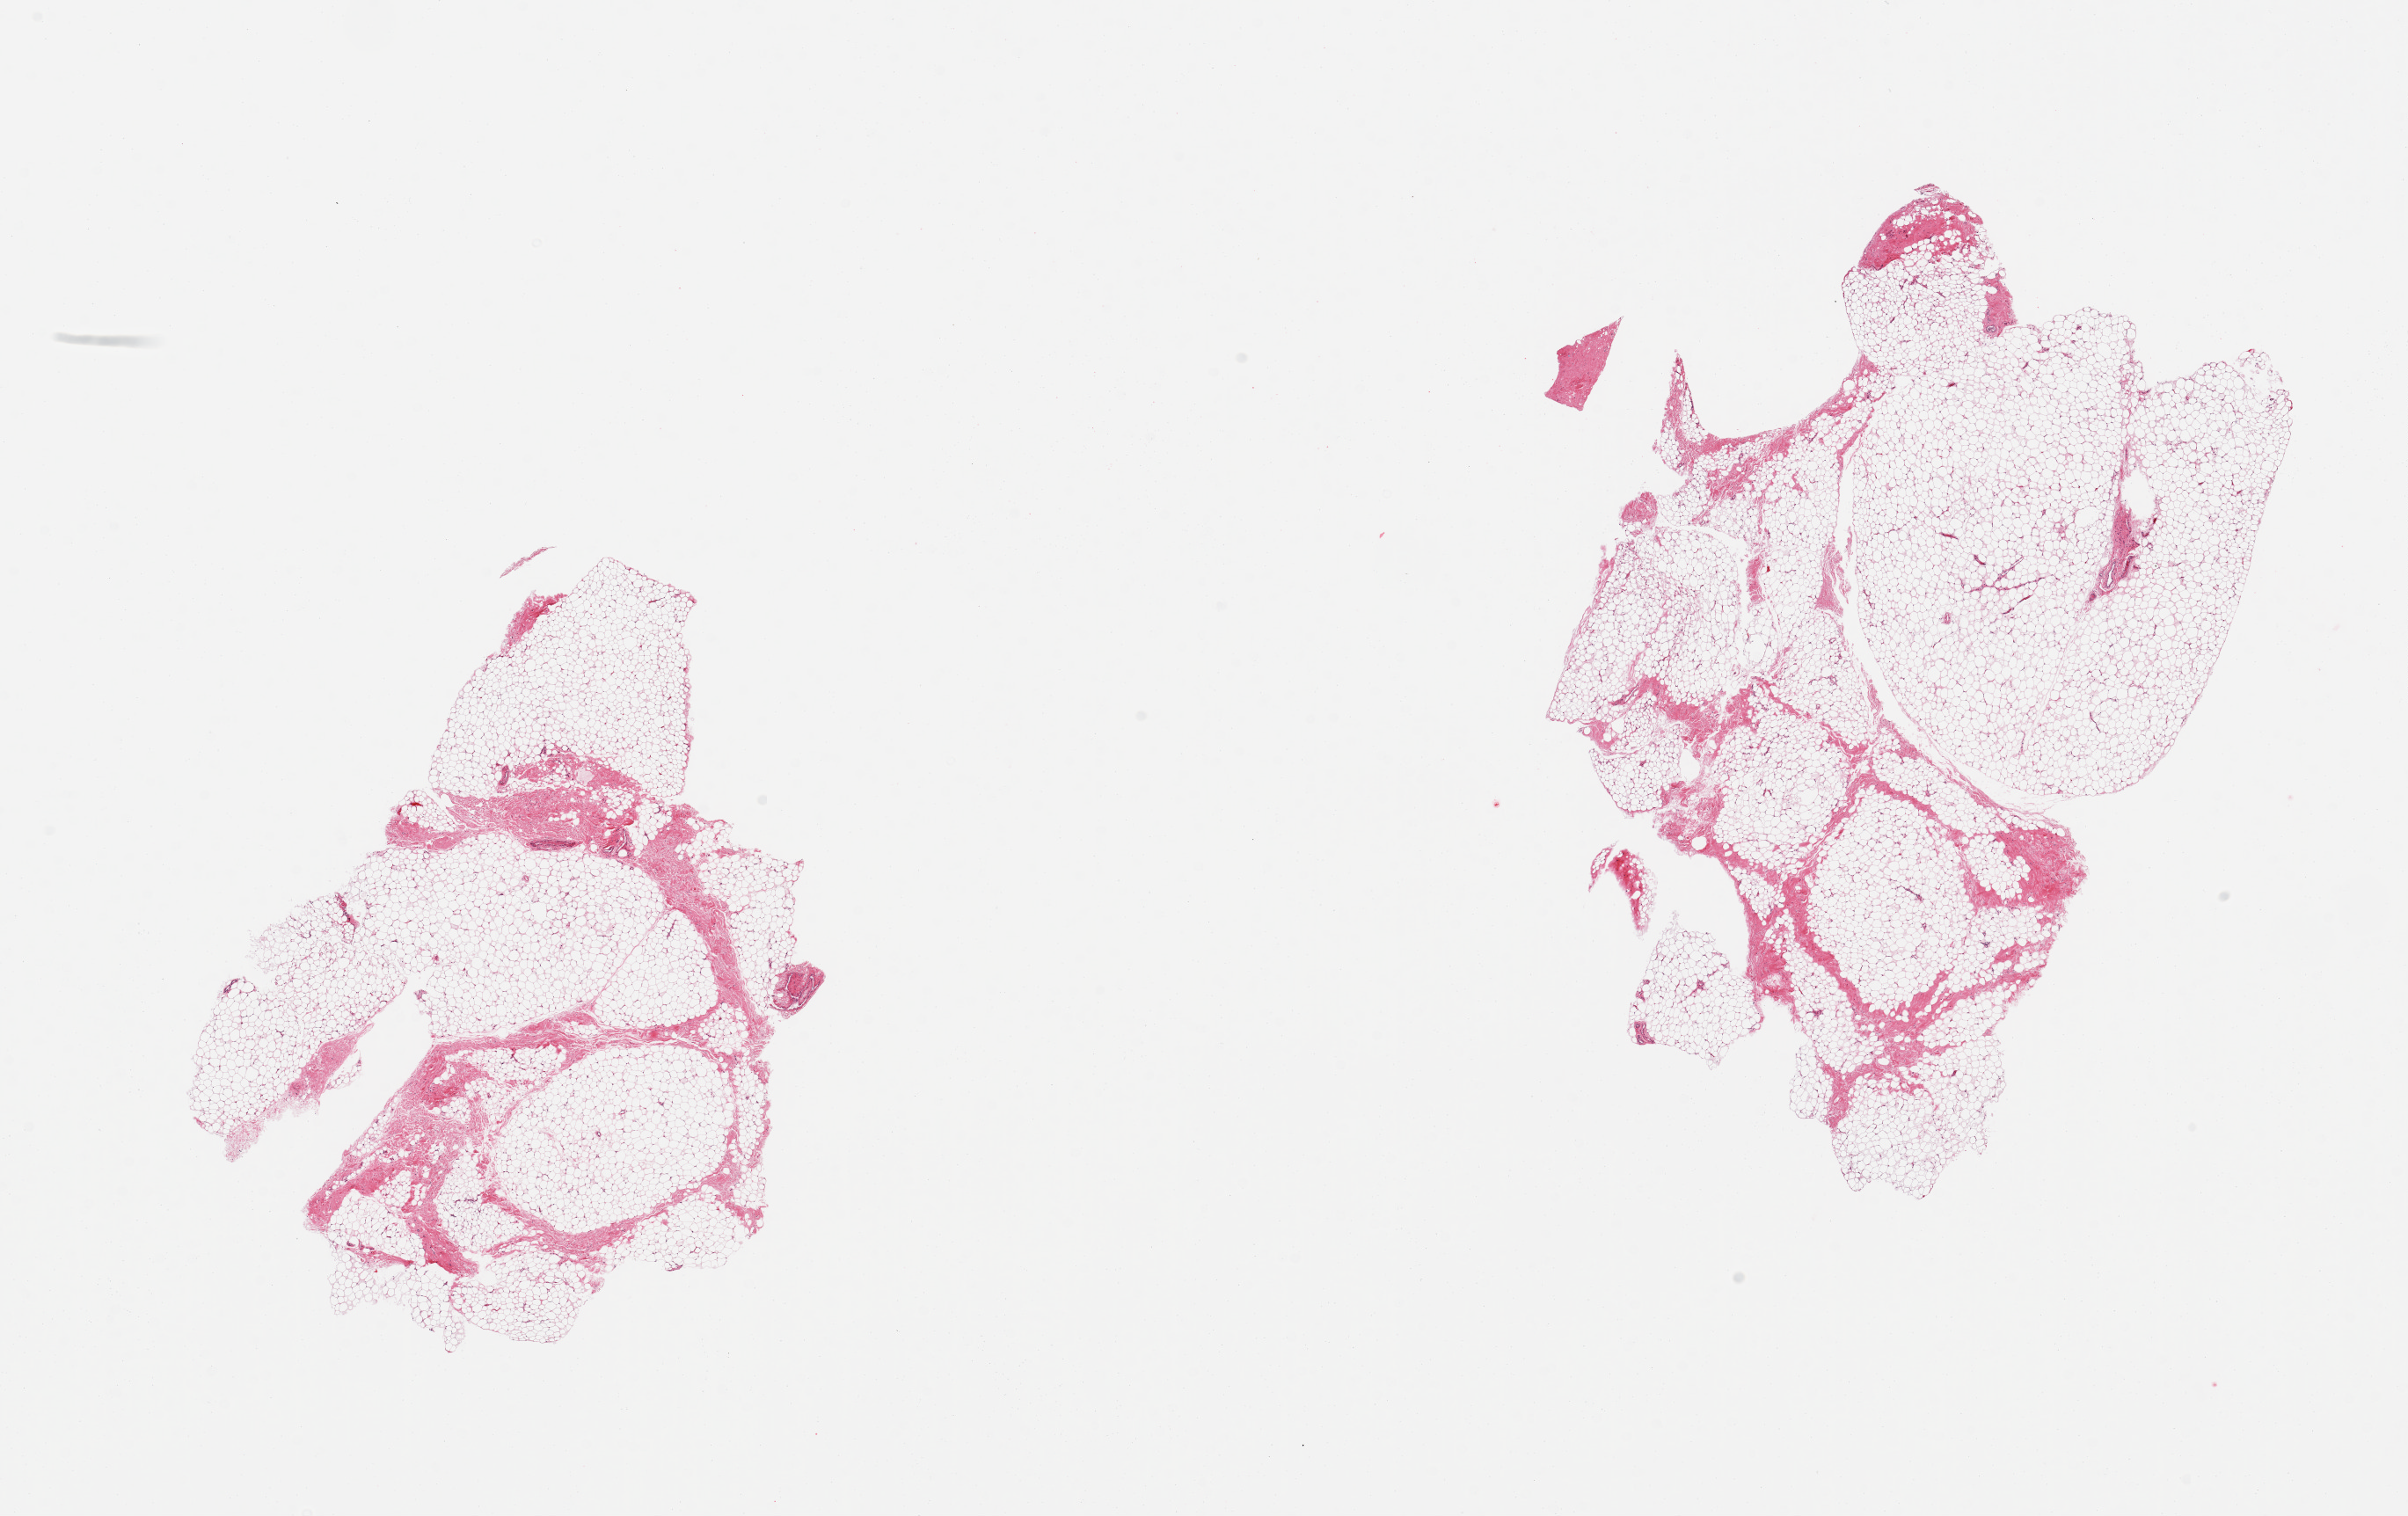
Digitized haematoxylin and eosin-stained section, whole scanned area (about 21.7 x 13.6 mm) shown as a low-resolution overview. PAXgene-fixed paraffin-embedded (PFPE) section. Target tissue: breast. Donor tissue sample. Male donor.
Pathologist's review note for this sample: 2 pieces; mostly fat with low fibrous content and no mammary ducts.